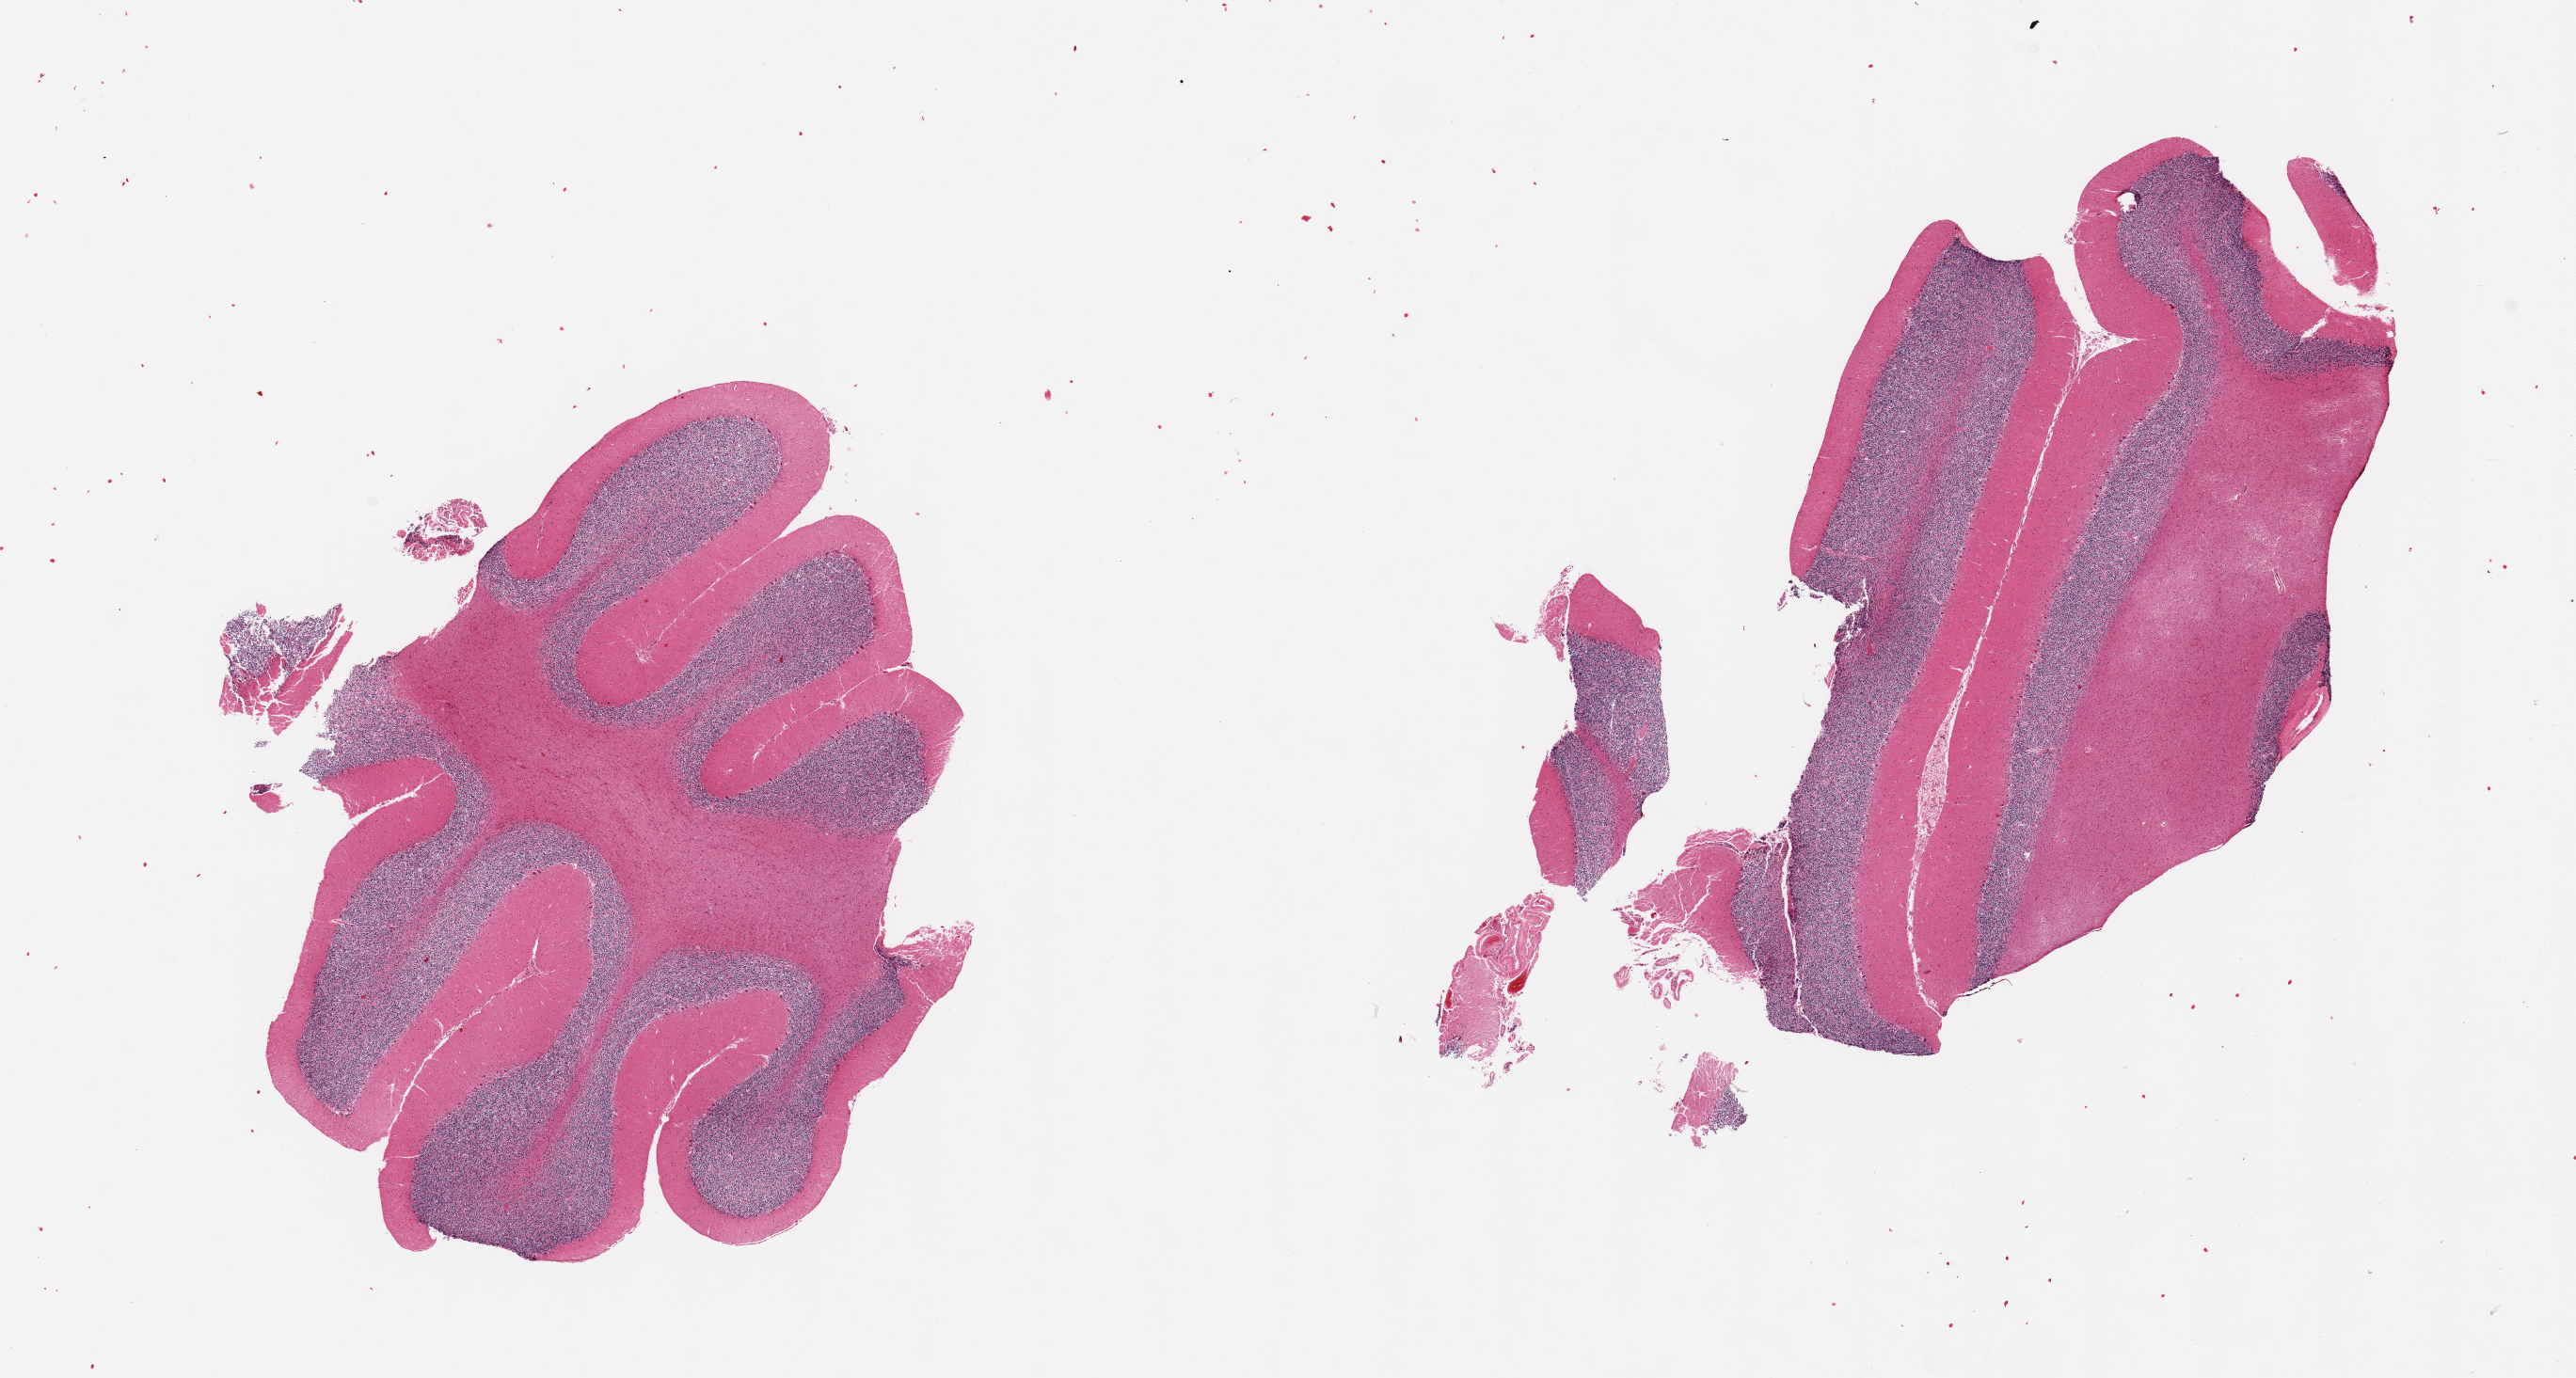
Whole-slide image, haematoxylin and eosin stain, whole scanned area (about 21.7 x 11.6 mm, acquisition: 20x scan) shown as a low-resolution overview. PAXgene-fixed paraffin-embedded (PFPE) section. Target tissue: cerebellum. Donor tissue sample. Donor sex: male.
Reviewer comment on this tissue sample: 2 fragmented pieces; focal reduction in Purkinje cells.